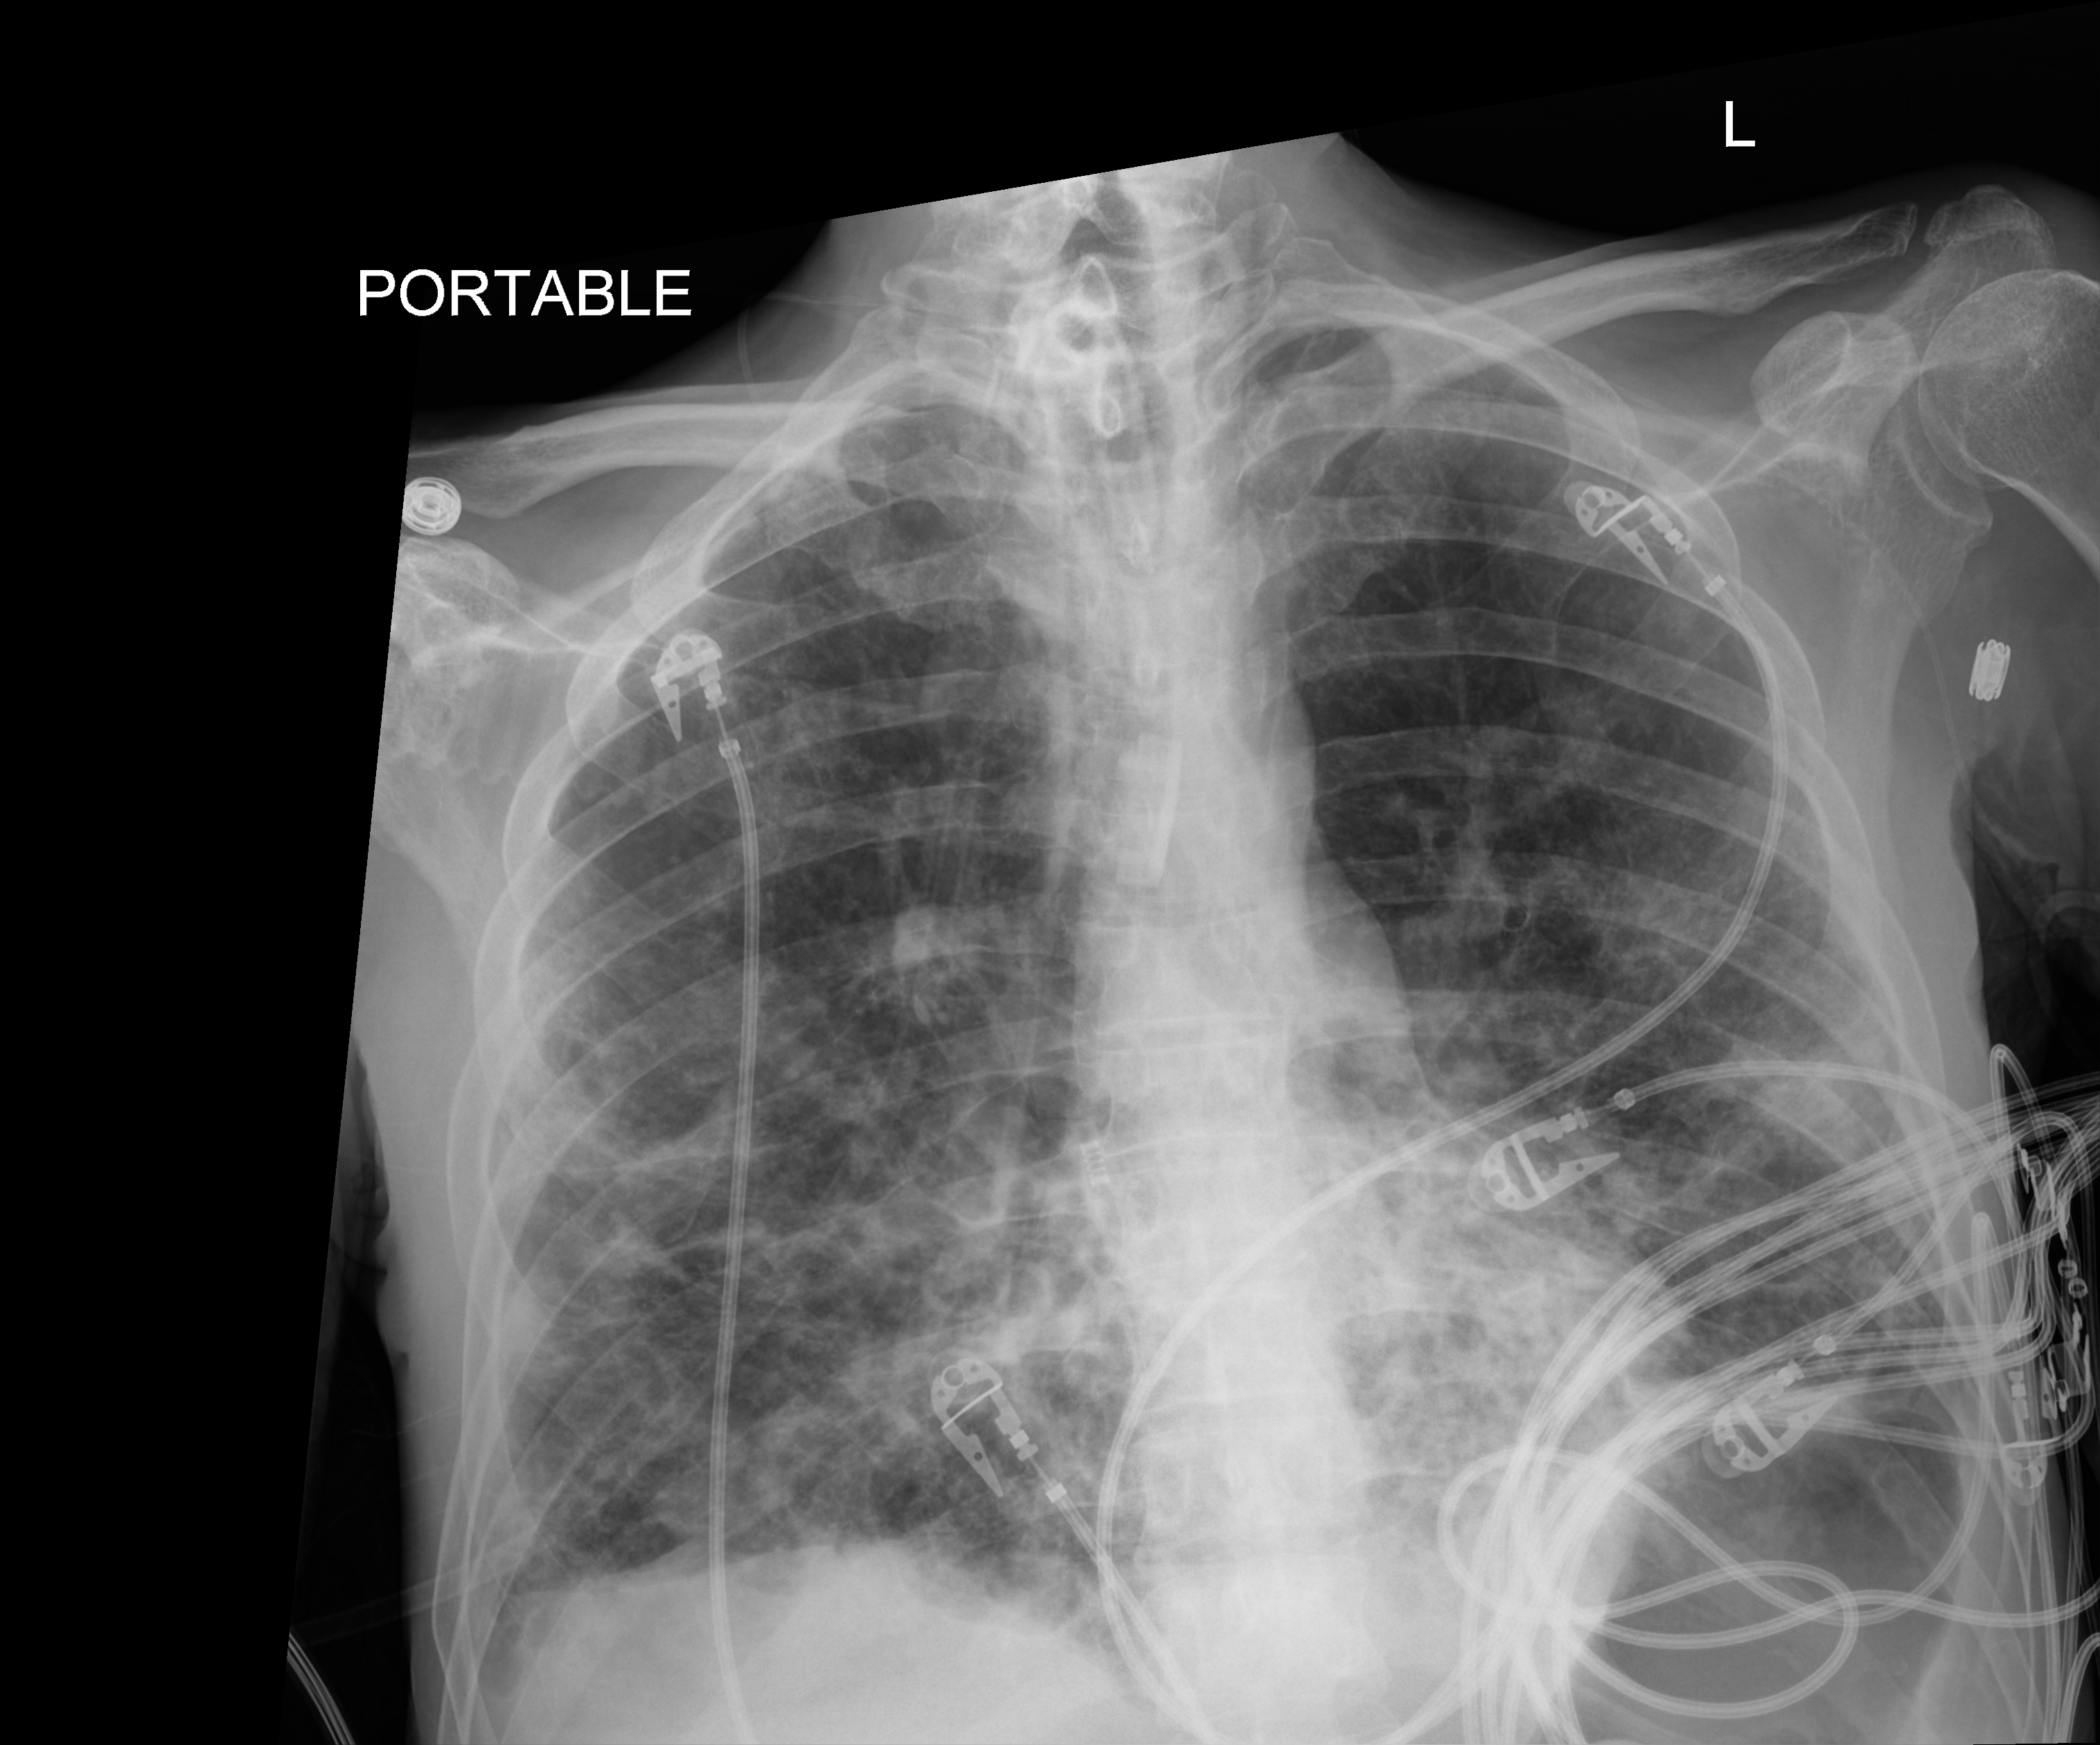
Chest X-ray; anteroposterior (AP) projection. Male patient hospitalised with COVID-19, age 18–59 years.
Admission-level facts for this patient (not findings on this image; timing relative to this image not recorded):
- length of hospital stay: 96 days
- admitted to intensive care during this hospital stay: yes